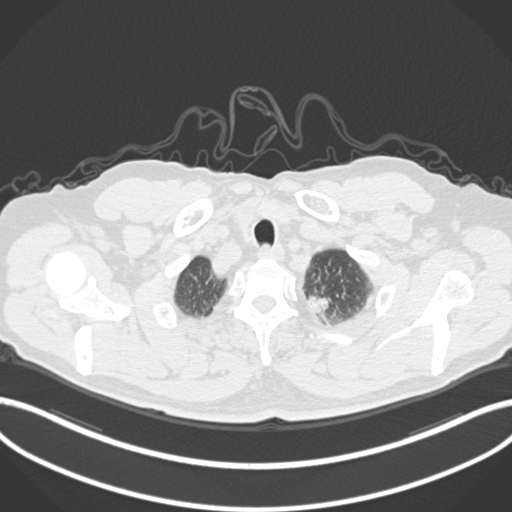
Chest CT, one axial slice; slice 294 of 306 in the series (ordered by position); reconstruction kernel B30f; 120 kVp; lung window (W 1500 / L -600 HU); 1 mm slice thickness; 512 × 512 image matrix, field of view 400 × 400 mm. Male patient, age 64 years. Case-level facts recorded for this patient, not image findings: clinical TNM (as recorded): T1c N0 M0.
Structures marked on this image (bounding box drawn by a radiologist):
- lung tumour (recorded histology: adenocarcinoma): bounding box (x1, y1, x2, y2) in pixels: (303, 288, 337, 322)